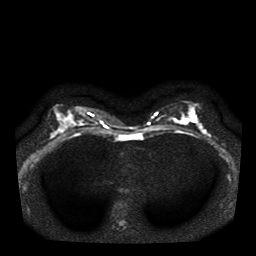
Breast MRI, one axial slice. Slice 20 of 41 in the series (ordered by position). Diffusion-weighted series; image 2 of 4 stored at this slice position (different b-values; order by instance number). 1.5 T. 256 × 256 image matrix. Female patient.
Outlined on this slice (outlined manually by an expert reader):
- tumour on diffusion-weighted imaging: bounding box [x1, y1, x2, y2] px = [190, 115, 197, 123]